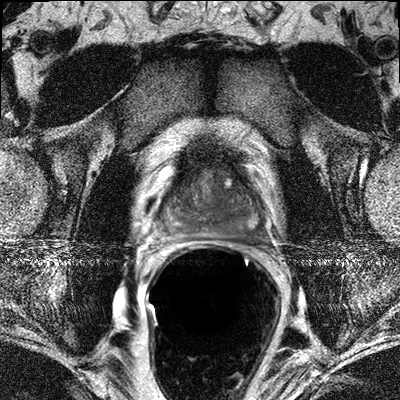
Multiparametric prostate MRI examination; 3 images, each a single mid-volume slice chosen by position (not for content). Treatment context recorded for this patient: Surgery.
Image 1: T2-weighted axial slice, series "T2W_TSE_AX", slice 17 of 32, 3 mm slice thickness.
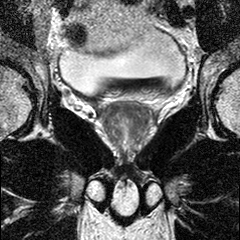
Image 2: T2-weighted coronal slice, series "T2W_TSE_COR", slice 13 of 24, 3 mm slice thickness.
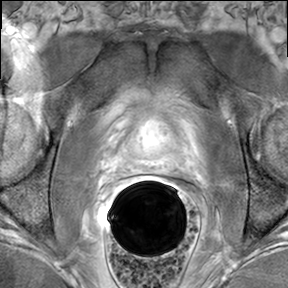
Image 3: DCE (dynamic gadolinium-enhanced) axial slice, slice 17 of 32, dynamic phase 5 of 8.
Report of this MRI examination:
FINDINGS: The prostate has a maximal lateral diameter of 4.5 cm, a maximal craniocaudal diameter of 3.9 cm and a maximal AP diameter of 3.4 cm resulting in an estimated gland volume of 31 cc. The zonal anatomy is preserved. Within the prostate base (upper third) with extension into the mid third and apical third there is diffuse T2-weighted signal alteration seen in the posterior and posterior lateral left peripheral zone and to a lesser extent in the right posterior peripheral zone (paramedian right) between 3 and 7 o'clock. Within these areas there is suspicious contrast enhancement seen, with rapid wash-in and wash-out pattern. These findings are suggestive for bilateral prostate cancer with dominant nodule in the left upper third. The dominant nodule on the left measures 1.7 x 1.1 cm. No evidence for involvement of the neurovascular bundle on either side. No evidence for seminal vesicles infiltration. No evidence of involvement of bladder neck and rectal wall. No suspiciously enlarged obturator and iliac lymph nodes. Multiplanar reconstructions, subtraction images, and CAD analysis of the dynamic series for assessment of the kinetic information facilitated the interpretation of the exam.
IMPRESSION: Bilateral prostate cancer with left-sided dominance, without evidence of extraglandular extension. The dominant nodule in the left prostate base measuring max. 1.7 cm. No evidence of neurovascular bundle involvement on either side, or seminal vesicles infiltration. No pelvic lymphadenopathy on MRI

Biopsy pathology report for this patient (as recorded):
The specimen consists of multiple core fragments of tan soft tissue measuring 0.3cm to 1.5cm in length and 0.1cm in diameter. The specimen is submitted in seven cassettes.1-right pz, 2-right pz/tz, 3-right apex, 4-left pz, 5-left pz/tz, 6-left apex, 7-free floater. PROSTATE: 1. RIGHT PZ: PROSTATIC ADENOCARCINOMA, GLEASON SCORE 3+3=6/10, INVOLVING 10% OF TISSUE. CHRONIC INFLAMMATION PRESENT. 2. RIGHT PZ: PROSTATIC ADENOCARCINOMA, GLEASON SCORE 3+3=6/10, INVOLVING <1% OF TISSUE. 3. RIGHT PZ/TZ: FIBROMUSCULAR TISSUE ONLY. 4. LEFT PZ: PROSTATIC ADENOCARCINOMA, GLEASON SCORE 3+3=6/10, INVOLVING 60% OF TISSUE. 5. LEFT PZ/TZ: FIBROMUSCULAR TISSUE ONLY. 6. LEFT APEX: PROSTATIC ADENOCARCINOMA, GLEASON SCORE 3+3=6/10, INVOLVING 5% OF TISSUE. 7. FLOATER: PROSTATIC ADENOCARCINOMA, GLEASON SCORE 3+3=6/10, INVOLVING LESS THAN 5% OF TISSUE.

Prostatectomy specimen pathology (as recorded; the surgery followed this MRI):
The specimen is received fresh in a single container labeled with the patient' s name, hospital number and "Prostate, Seminal Vesicles and Vas Deferens". The specimen consists of a prostate with attached left and right seminal vesicles and segments of vas deferens. The specimen weighs 48.4 grams and measures 4.5x4x4 cm in greatest dimensions. The right and left seminal vesicles measures 5x2x0.3 cm and 4x2x0.3 cm, respectively. The left vas deferens measures 2 cm in length and 0.5 cm in diameter. The right vas deferens measures 3 cm in length and 0.5 cm in diameter. The prostate is symmetrical and firm. The specimen is inked as follows: right aspect black and left aspect blue. The specimen is serially sectioned to reveal prostatic tissue. The entire specimen is submitted in thirty cassettes as follows: 1 and 2 apical margin, 3 bladder neck margin, 4 thru 9 right anterior aspect, 10 thru 15 right posterior aspect, 17 thru 21 left anterior aspect, 22 thru 28 left posterior aspect, 29 right vas deferens and seminal vesicle margin, 30 left vas deferens and seminal vesicle margin.
Final Diagnosis PROSTATE, SEMINAL VESICLES AND VAS DEFERENS: Procedure: Radical prostatectomy Prostate Size: 4.5x4x4cm Weight: 48.4g Lymph Node Sampling: No lymph nodes present Histologic Type: Adenocarcinoma (acinar, not otherwise specified) Histologic Grade: 3+4 = 7/10 Primary pattern: Grade 3 Secondary pattern: Grade 4 Tumor Quantitation: Proportion (percentage) of prostate involved by tumor: 15% Extraprostatic Extension: Not identified
Seminal Vesicle Invasion: Not identified Margins: Margins uninvolved by invasive carcinoma
Treatment Effect on Carcinoma: Not identified Lymph-Vascular Invasion: Not identified
Perineural Invasion: Present Additional Pathologic Findings: High-grade prostatic intraepithelial neoplasia (PIN), acute and chronic inflammation Pathologic Staging (pTNM) Primary Tumor (pT)
pT2c: Bilateral disease Regional Lymph Nodes (pN) pNx: Cannot be assessed
Specify: Number examined: 0 Number involved: 0 Distant Metastasis (pM) Not applicable
AJCC Pathologic Stage: (pT2c, pN0) Clinical diagnosis and History: Prostate cancer